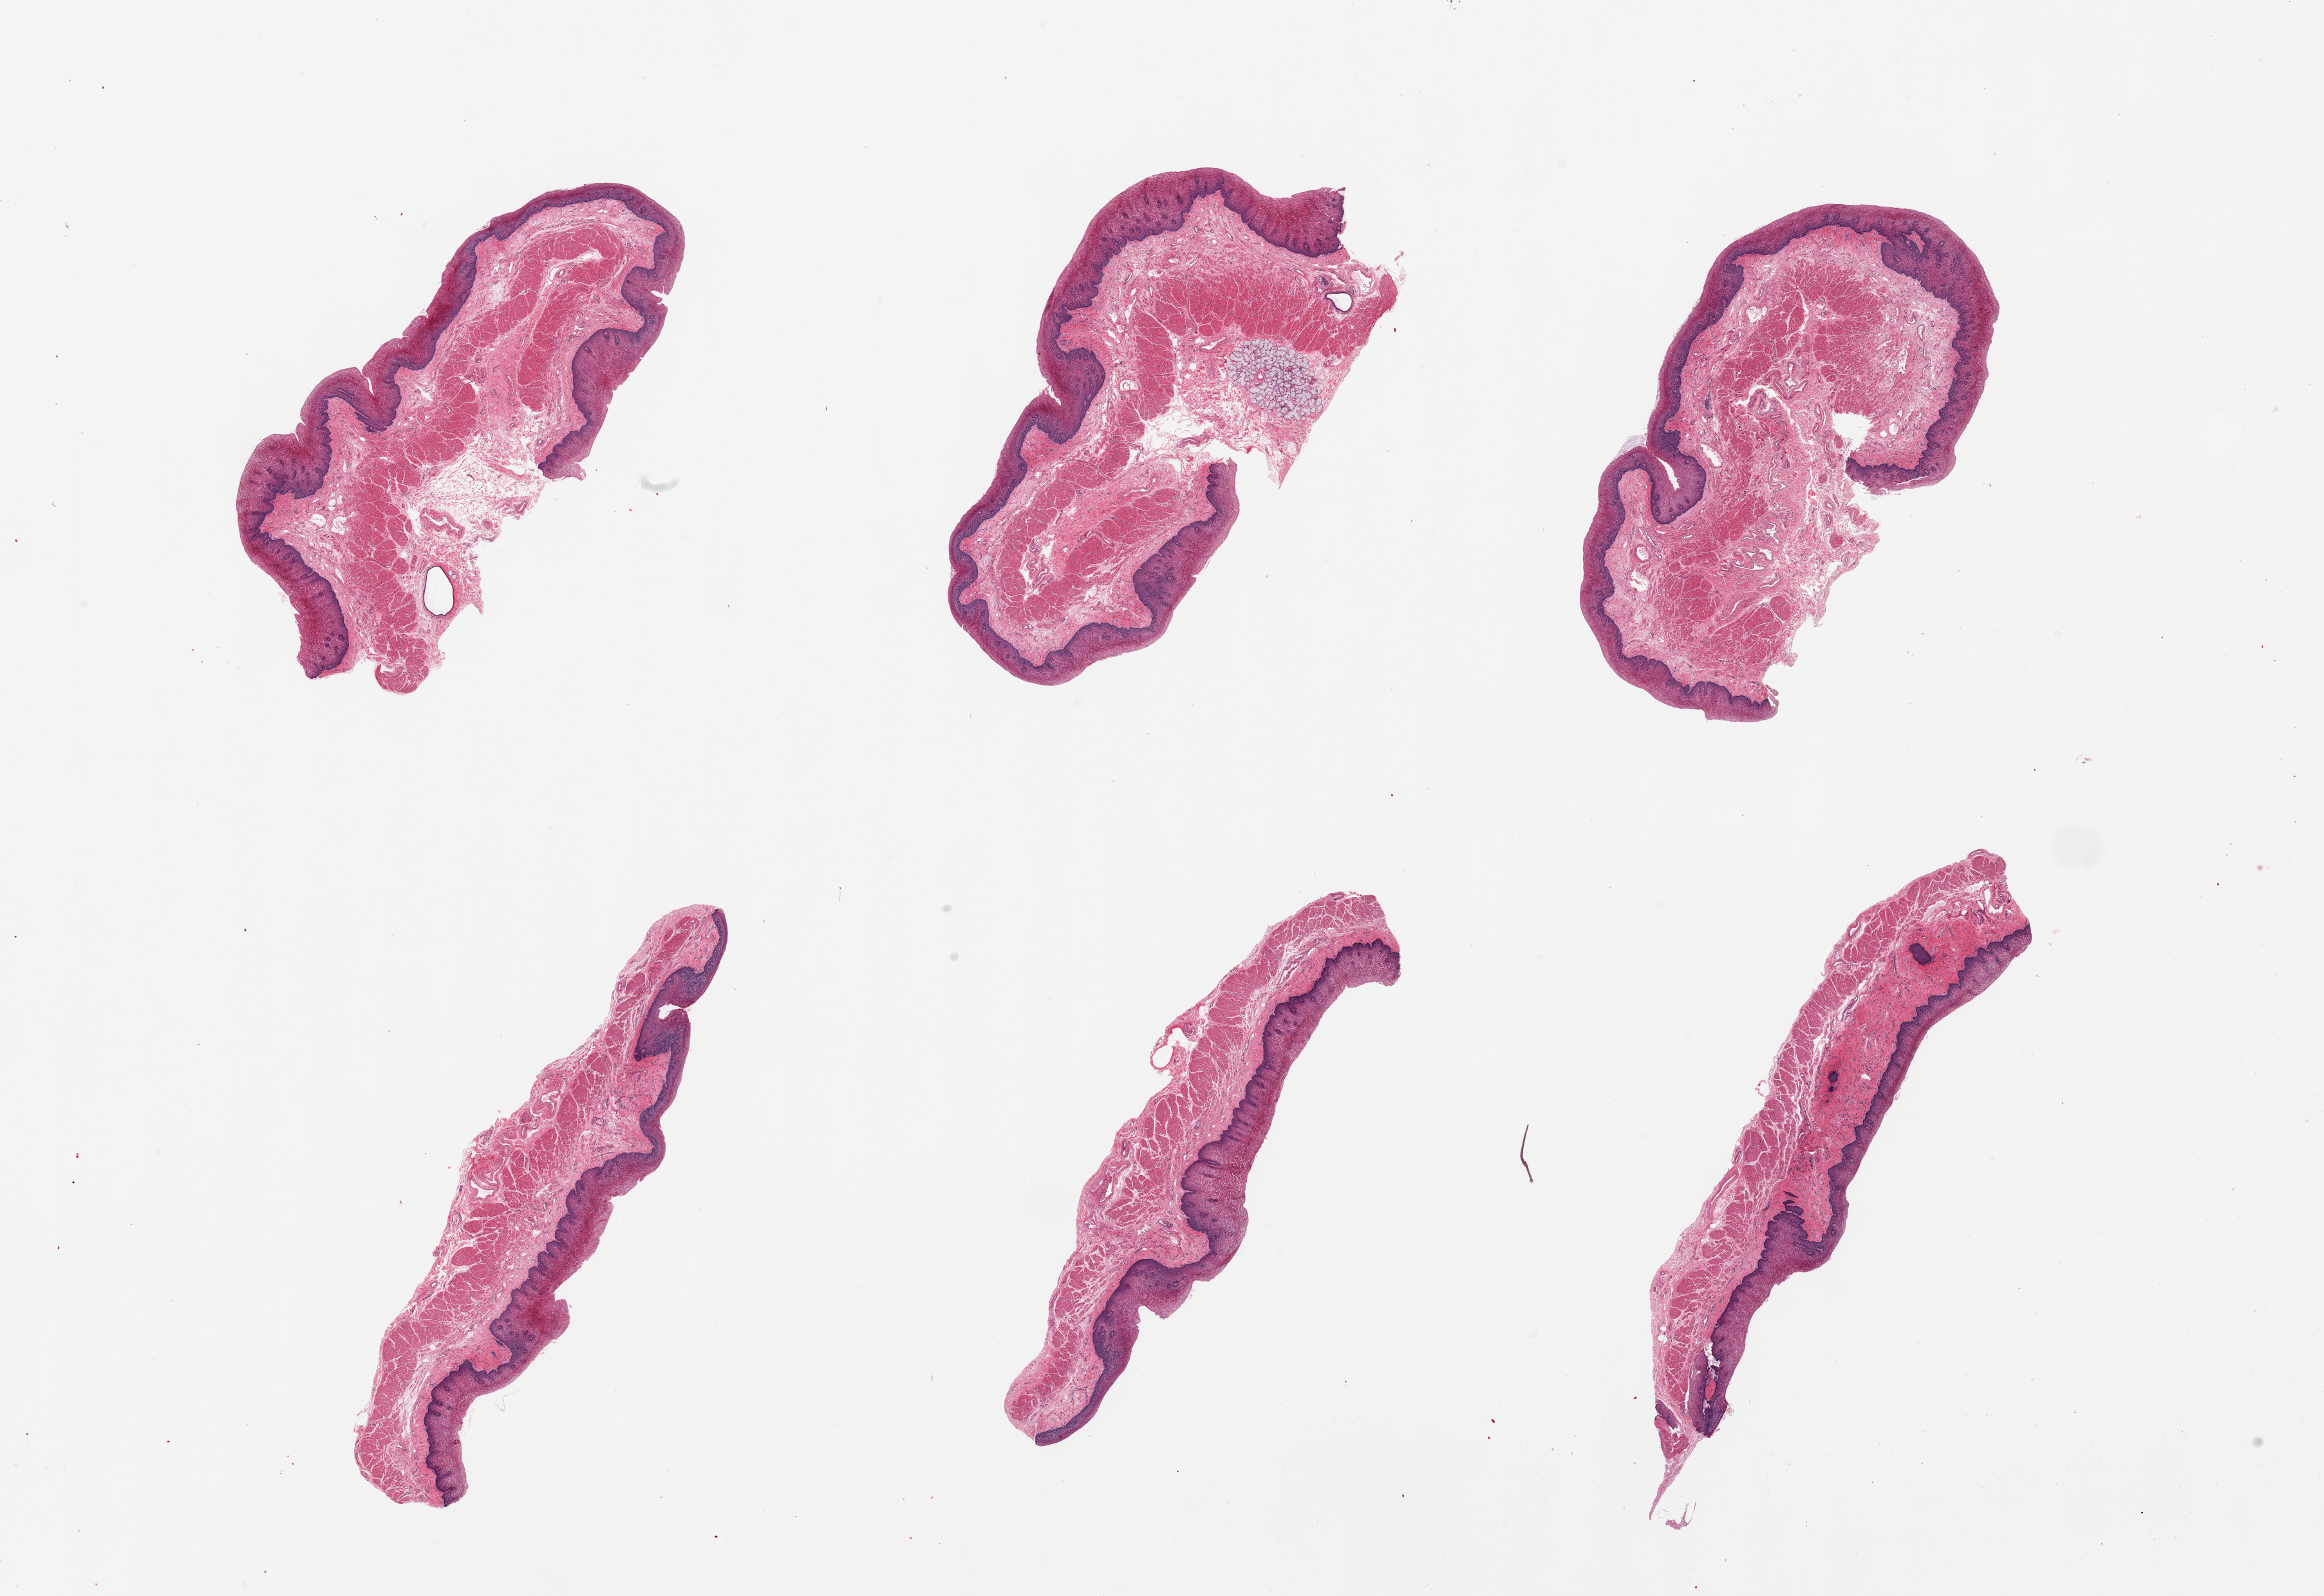
Whole-slide image, haematoxylin and eosin stain, whole scanned area (about 28.5 x 19.6 mm) shown as a low-resolution overview. PAXgene-fixed paraffin-embedded (PFPE) section. Sampled site (target tissue): esophageal mucous membrane. Tissue donor sample. Donor sex: female.
Reviewer comment on this tissue sample: 6 pieces. Well dissected.